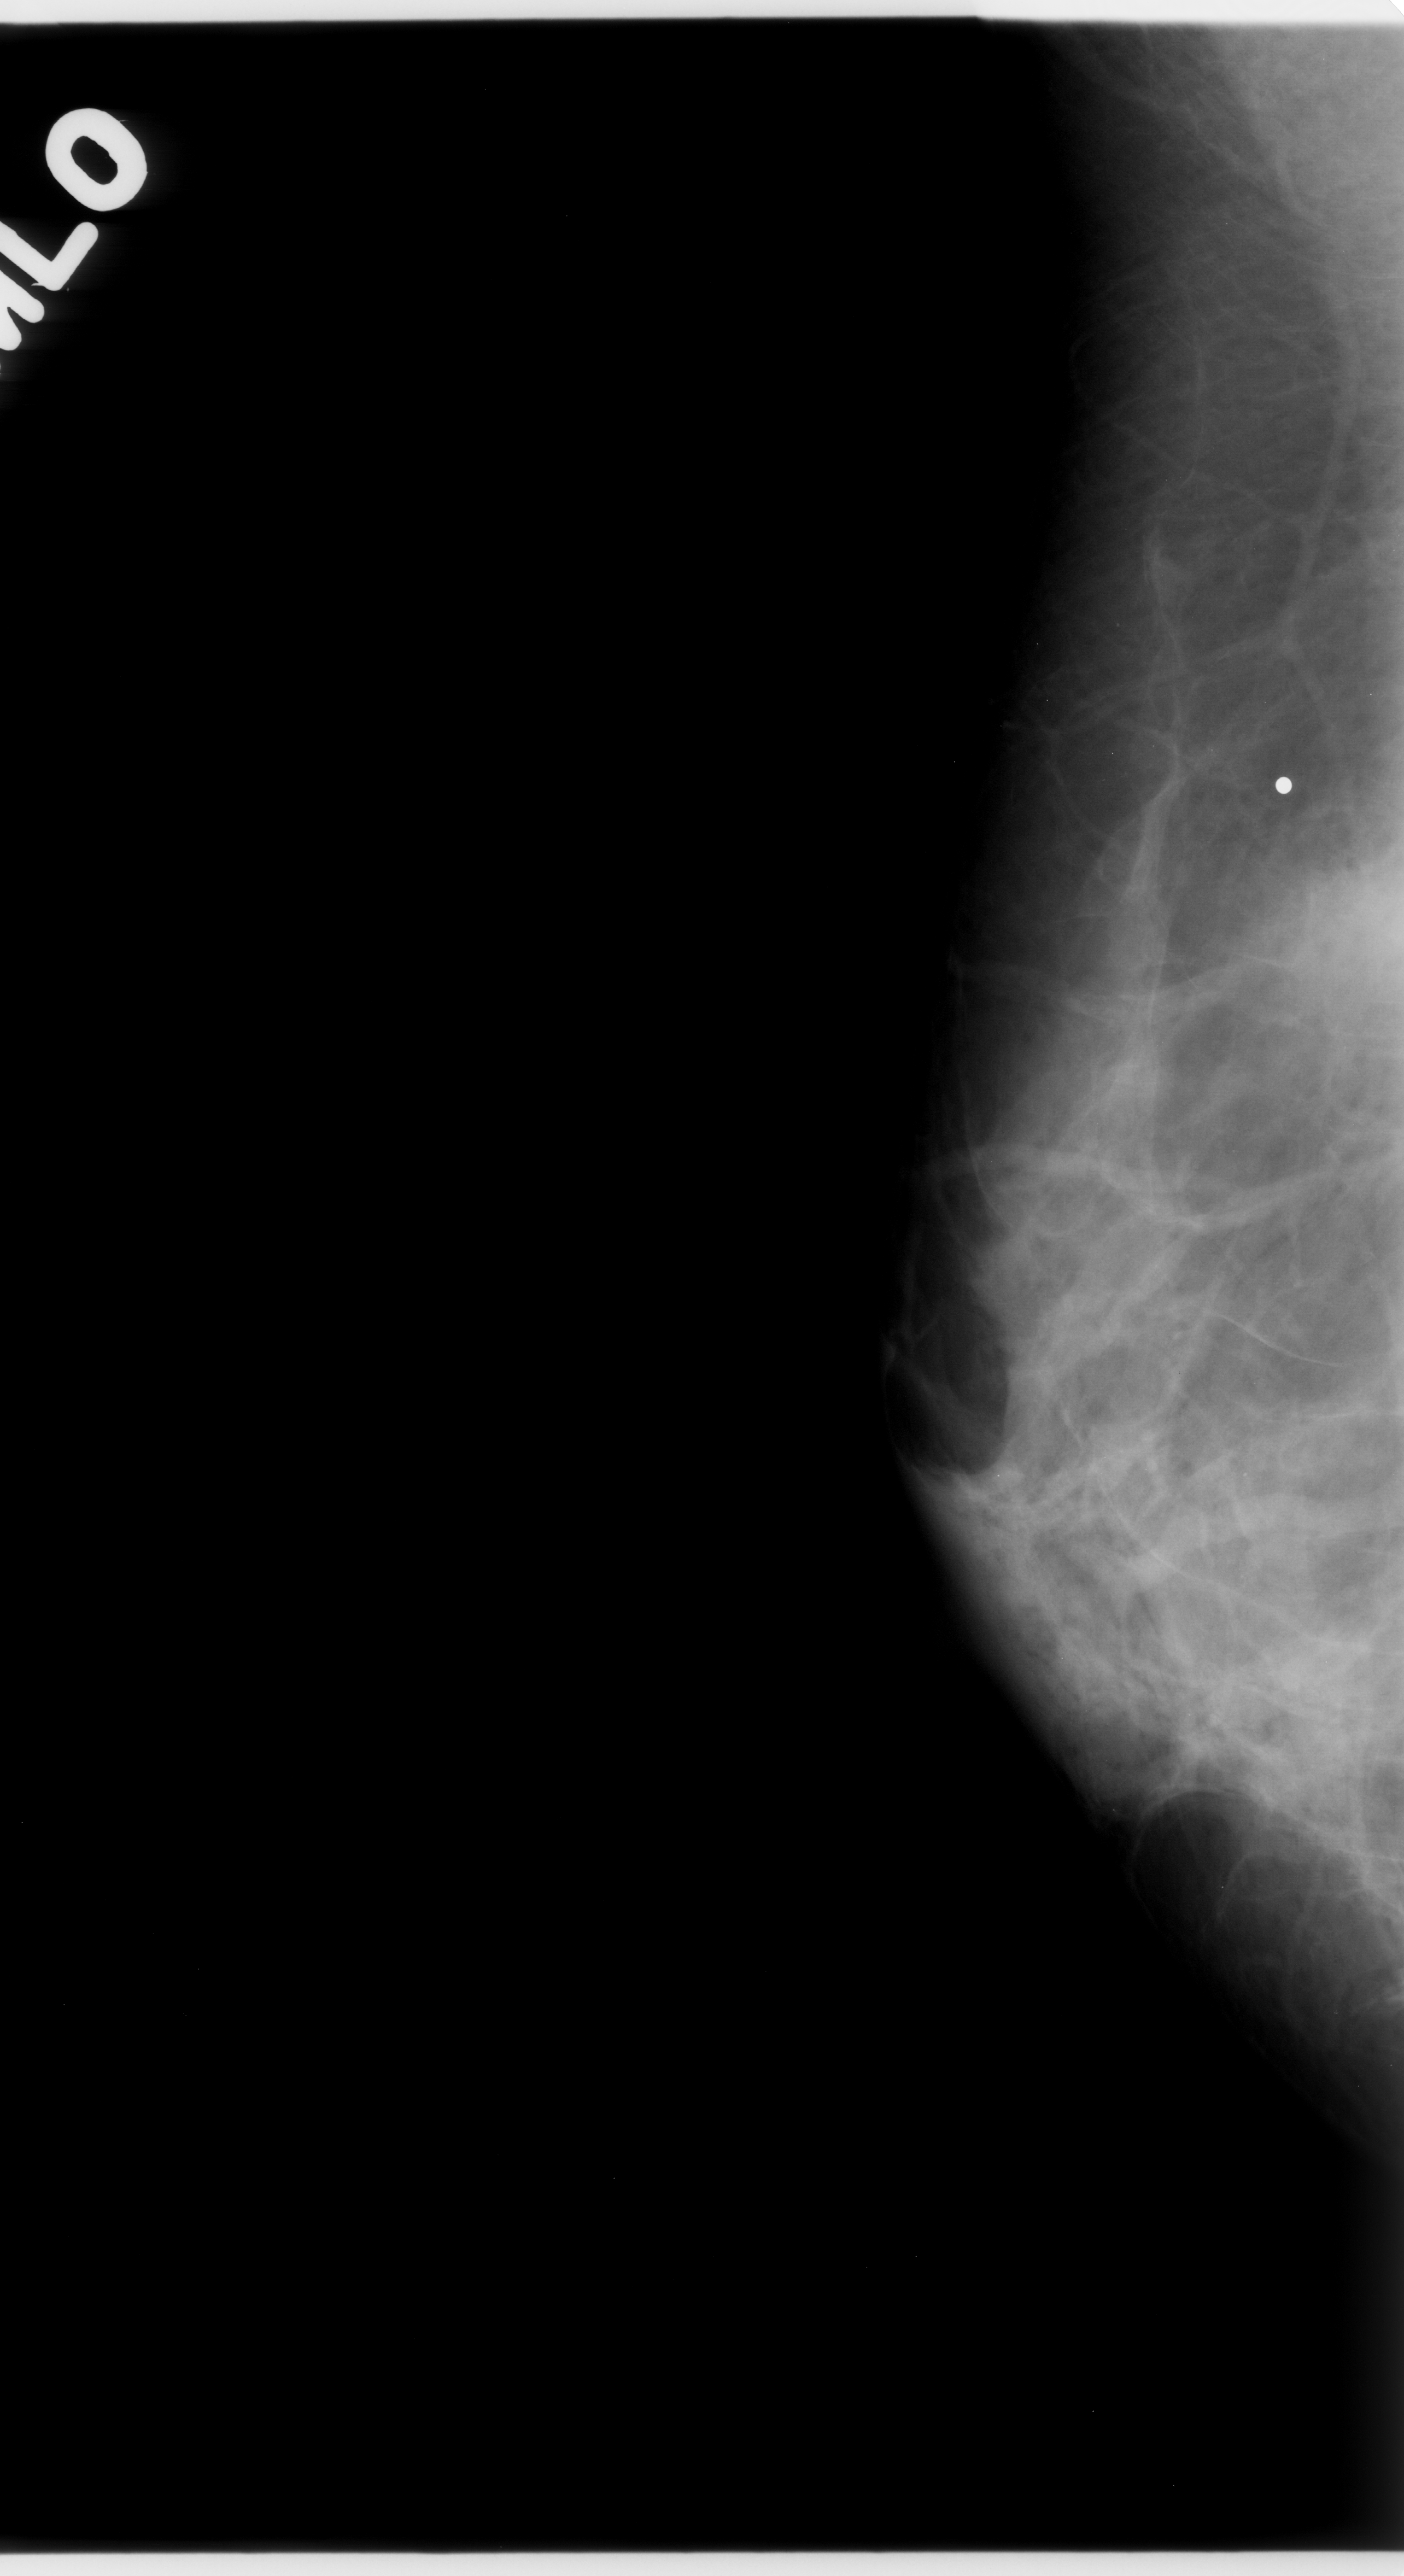
Scanned film-screen mammogram, right breast, mediolateral oblique (MLO) view, breast composition: scattered fibroglandular densities (BI-RADS density category 2 of 4).
Mass, shape oval, margins ill defined; BI-RADS assessment category 5; pathology (as recorded): malignant.